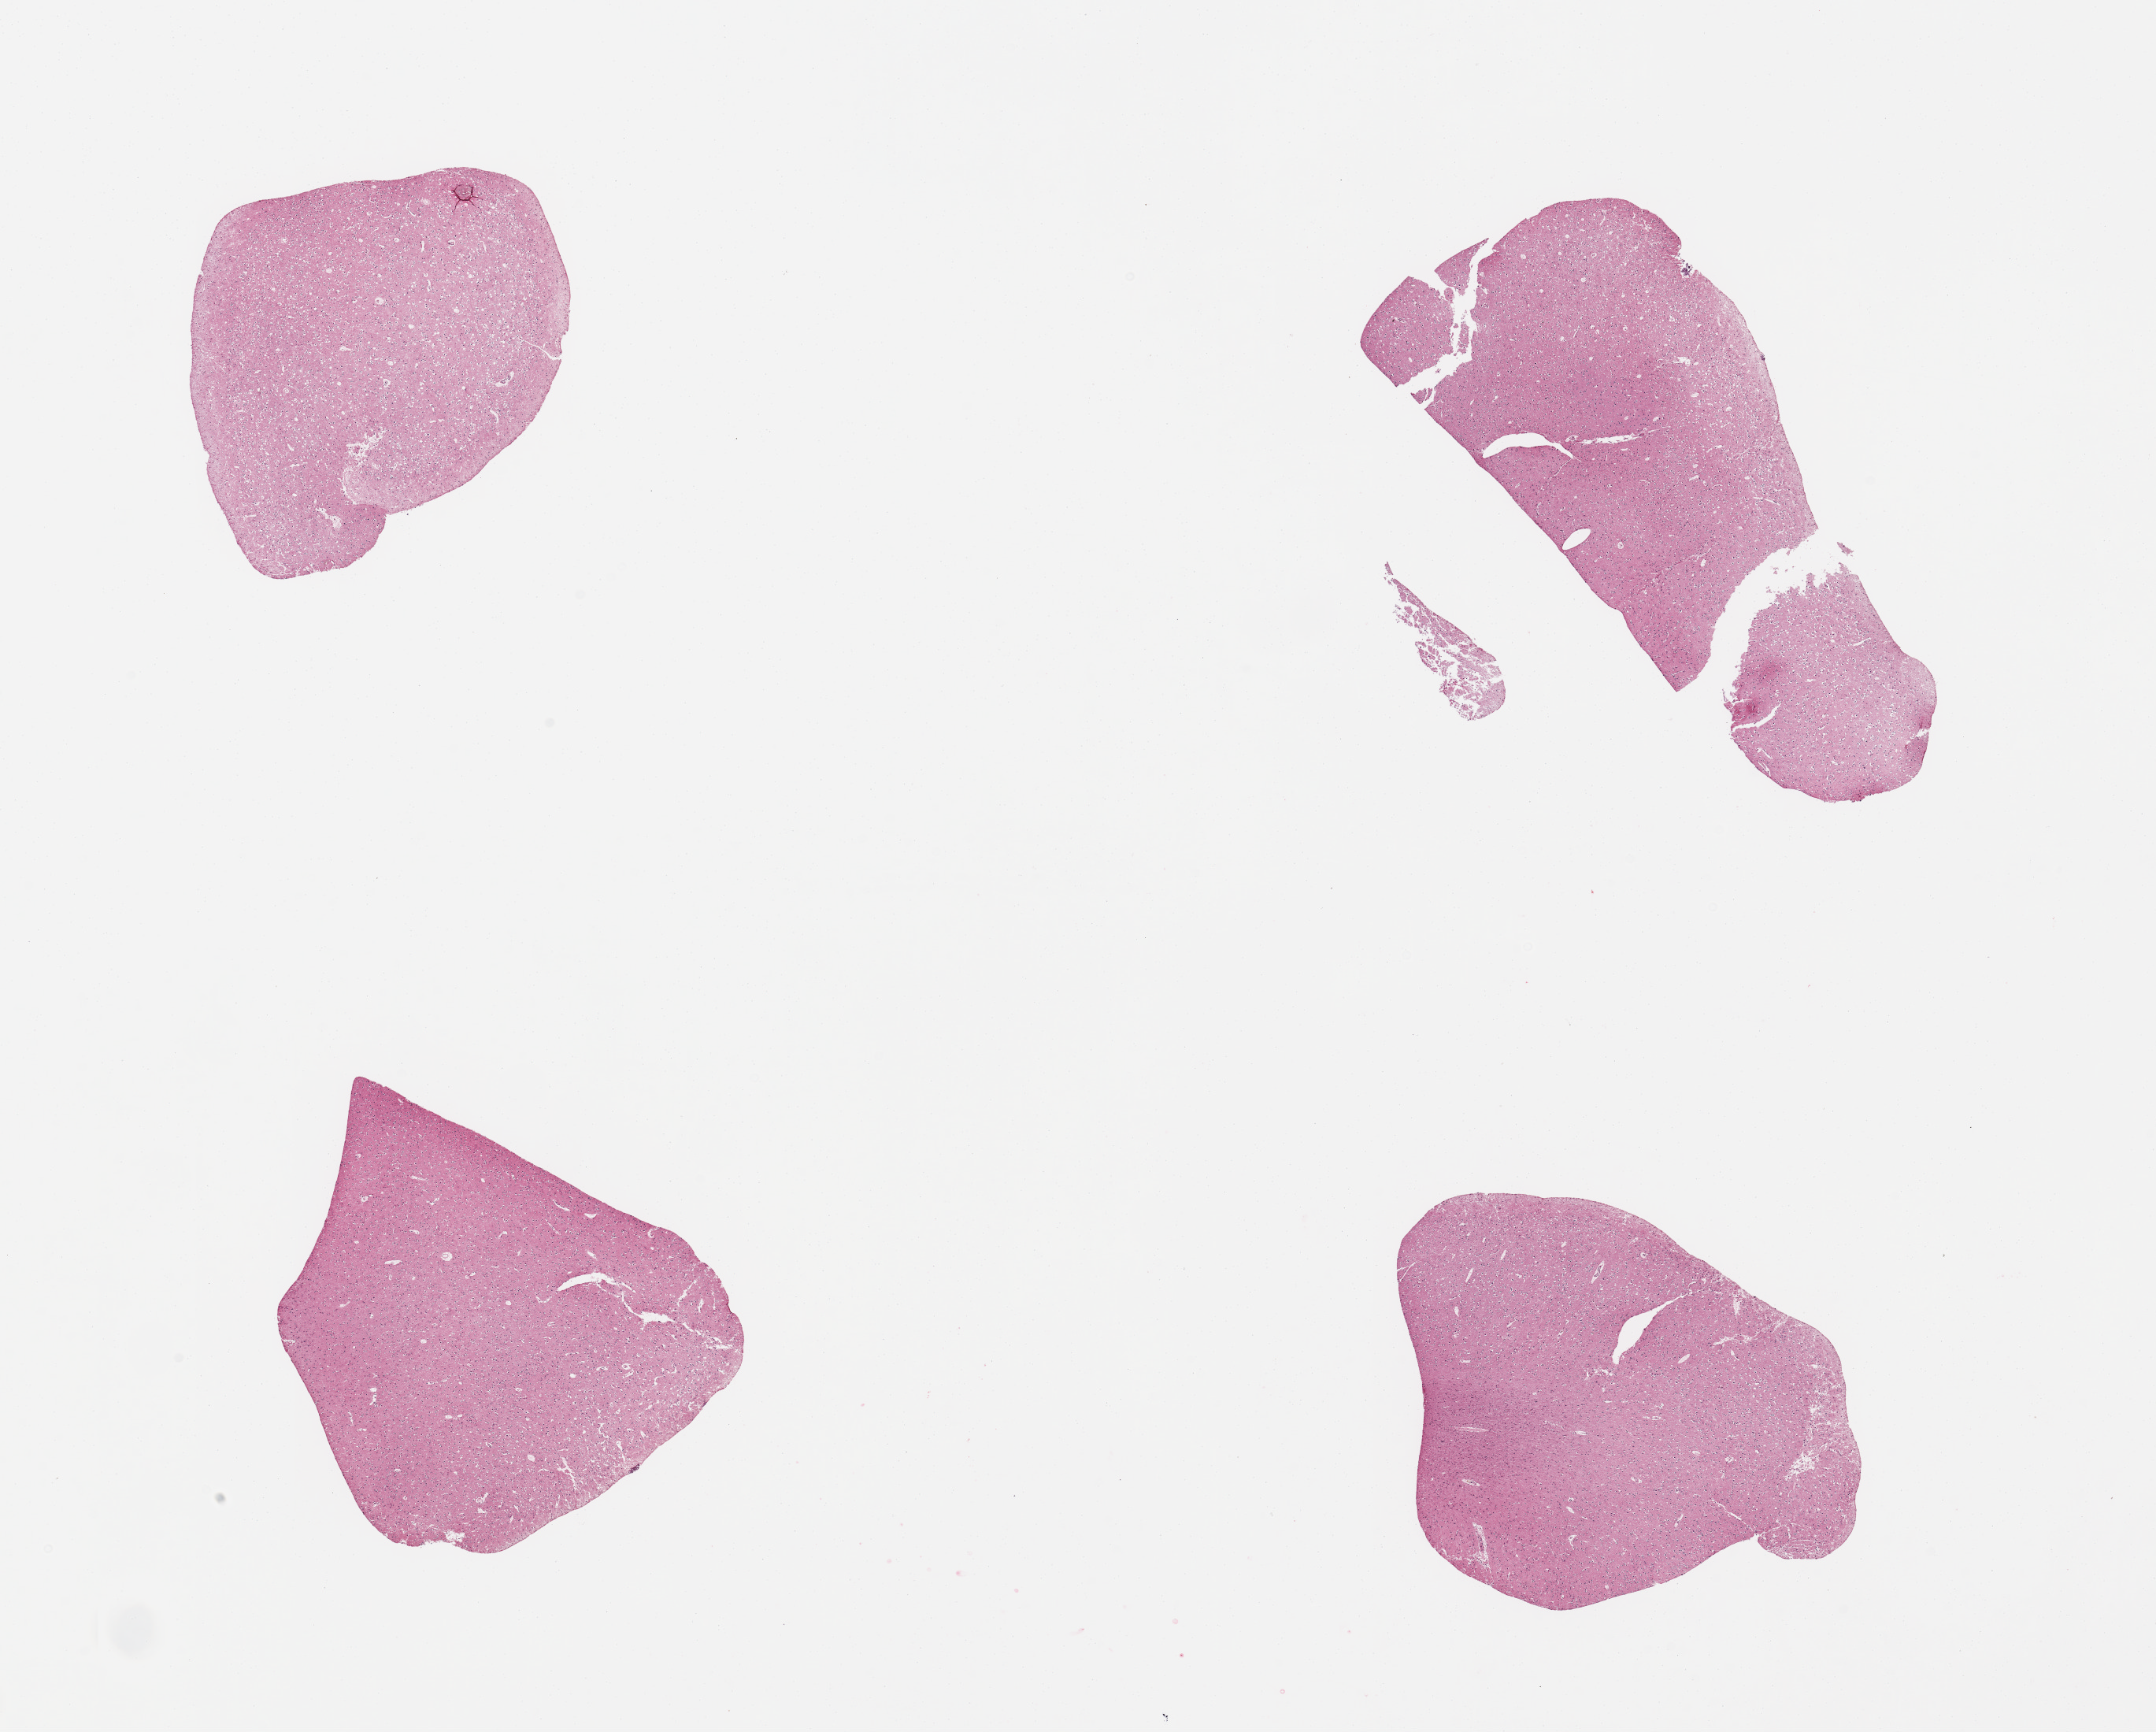
Digitized haematoxylin and eosin-stained section, brightfield — low-resolution overview of the scanned area, about 21.7 x 17.4 mm, PAXgene-fixed, paraffin-embedded tissue, sampled site (target tissue): cerebral cortex, tissue donor sample.
Pathologist's review note for this sample: 4 pieces, no abnormalities.